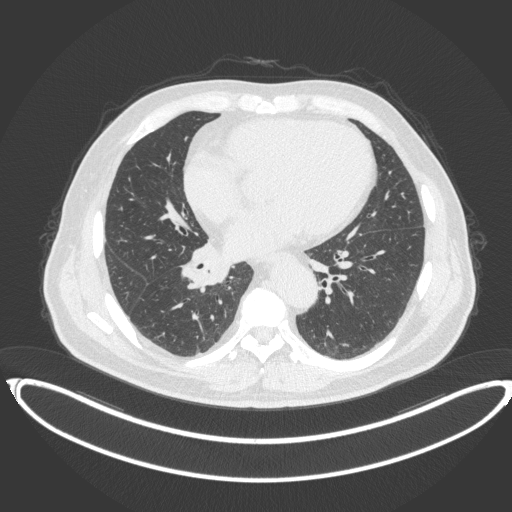
Chest CT, one axial slice. Reconstruction kernel B31f. 120 kVp. Lung window (W 1500 / L -600 HU). 512 × 512 image matrix, field of view 448 × 448 mm. Patient: male, 61 years. Case-level facts recorded for this patient, not image findings: clinical TNM (as recorded): T1b N1 M0.
Outlined on this slice (rectangle marked by the reading radiologist):
- lung tumour (recorded histology: squamous cell carcinoma): bounding box <178,243,229,295> (left, top, right, bottom; pixels)